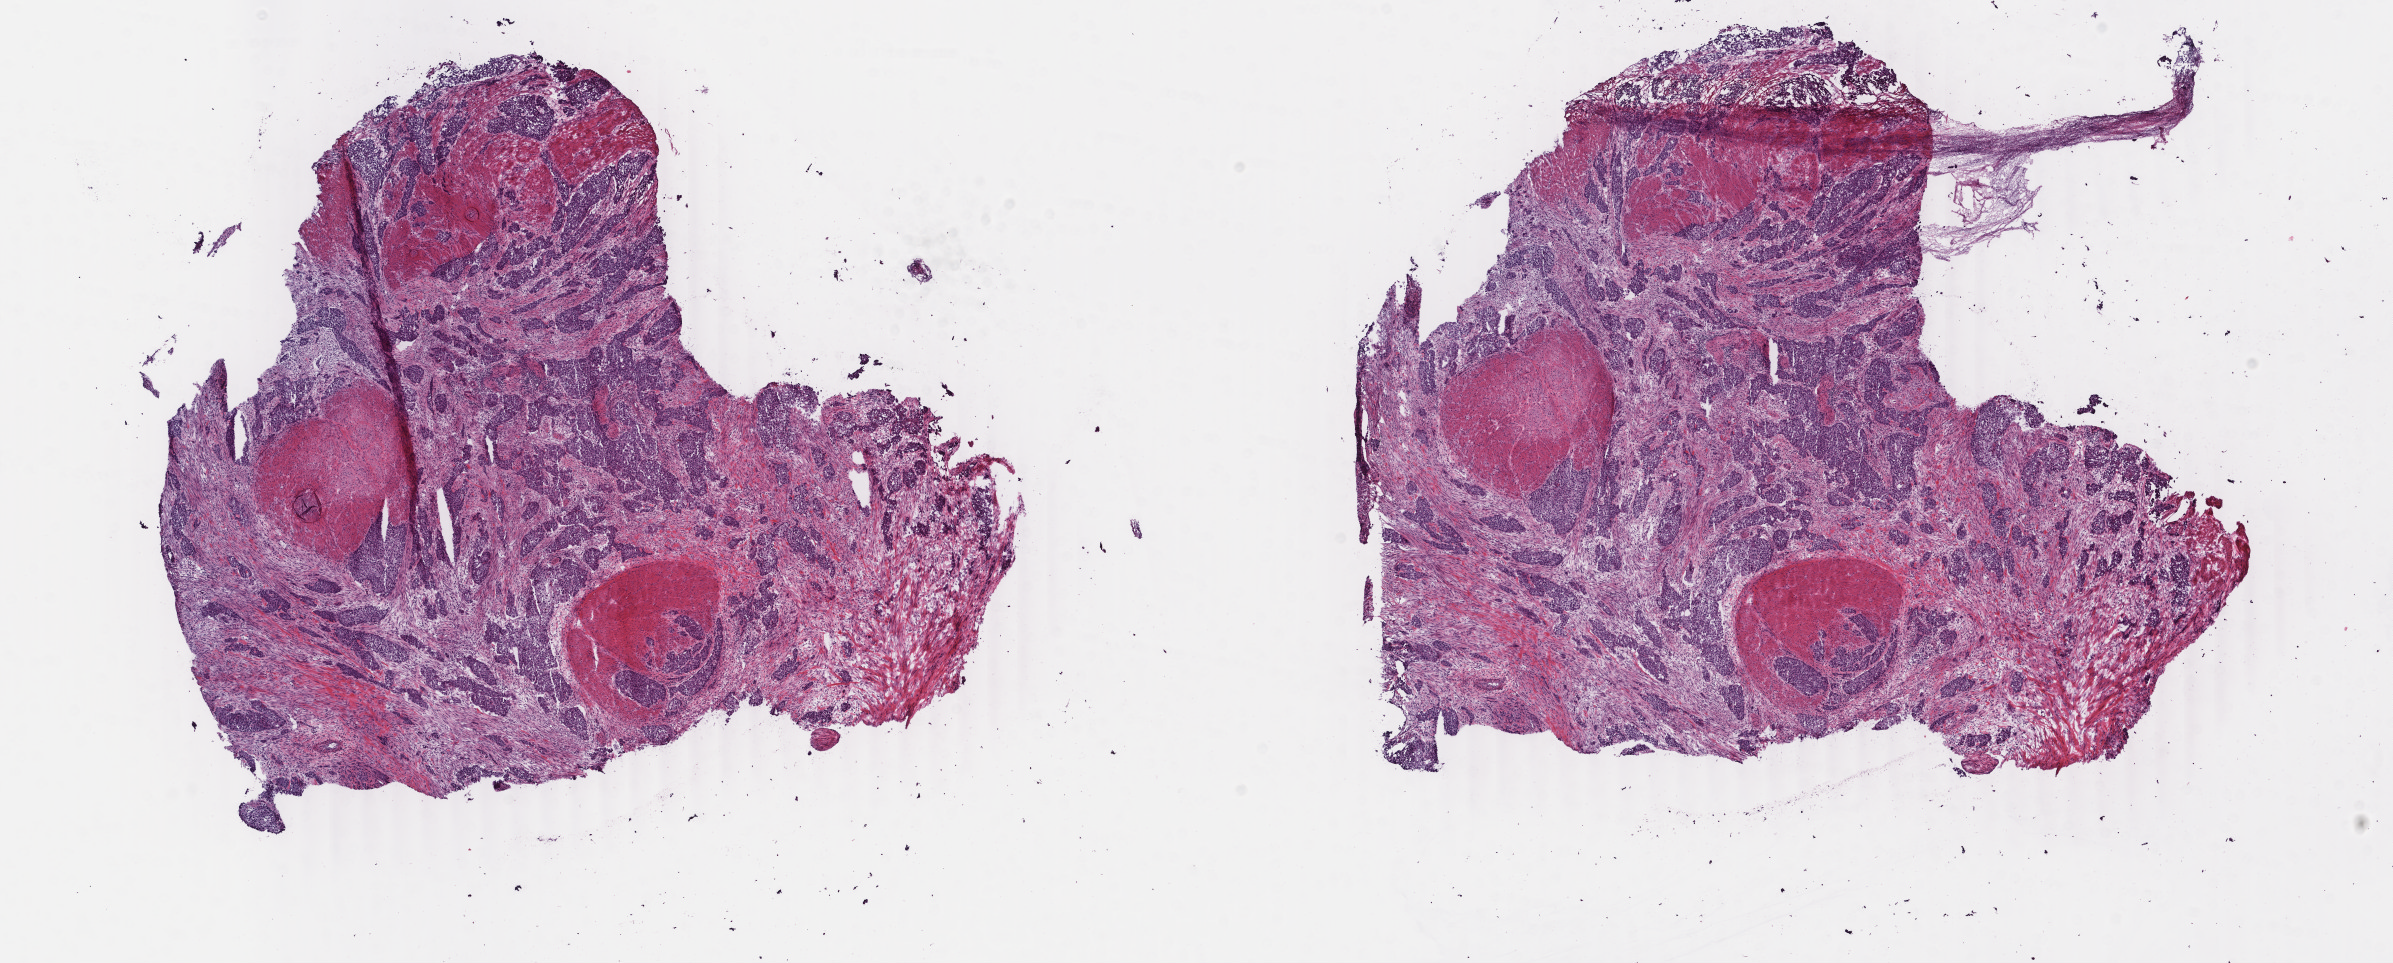
Digitized Hematoxylin and eosin (H&E) stained tissue section (whole slide) — a low-resolution overview of the entire scanned area, about 19.0 x 7.7 mm. Frozen section. Primary tumour sample from the bladder. Male, age 65 years at initial diagnosis. Histologic grade: high grade. Pathologist review of this section (percent, as recorded): tumour cells 65%, tumour nuclei 84%, normal cells 0%, stromal cells 35%, necrosis 0%. Infiltration values recorded for this section: lymphocyte infiltration 3%, monocyte infiltration 0%, neutrophil infiltration 0%.
TNM: T4 N2 M0. Histologic diagnosis: Transitional cell carcinoma (posterior wall of bladder). Lymph nodes positive (case pathology): 2 of 11 examined. AJCC pathologic stage: IV.